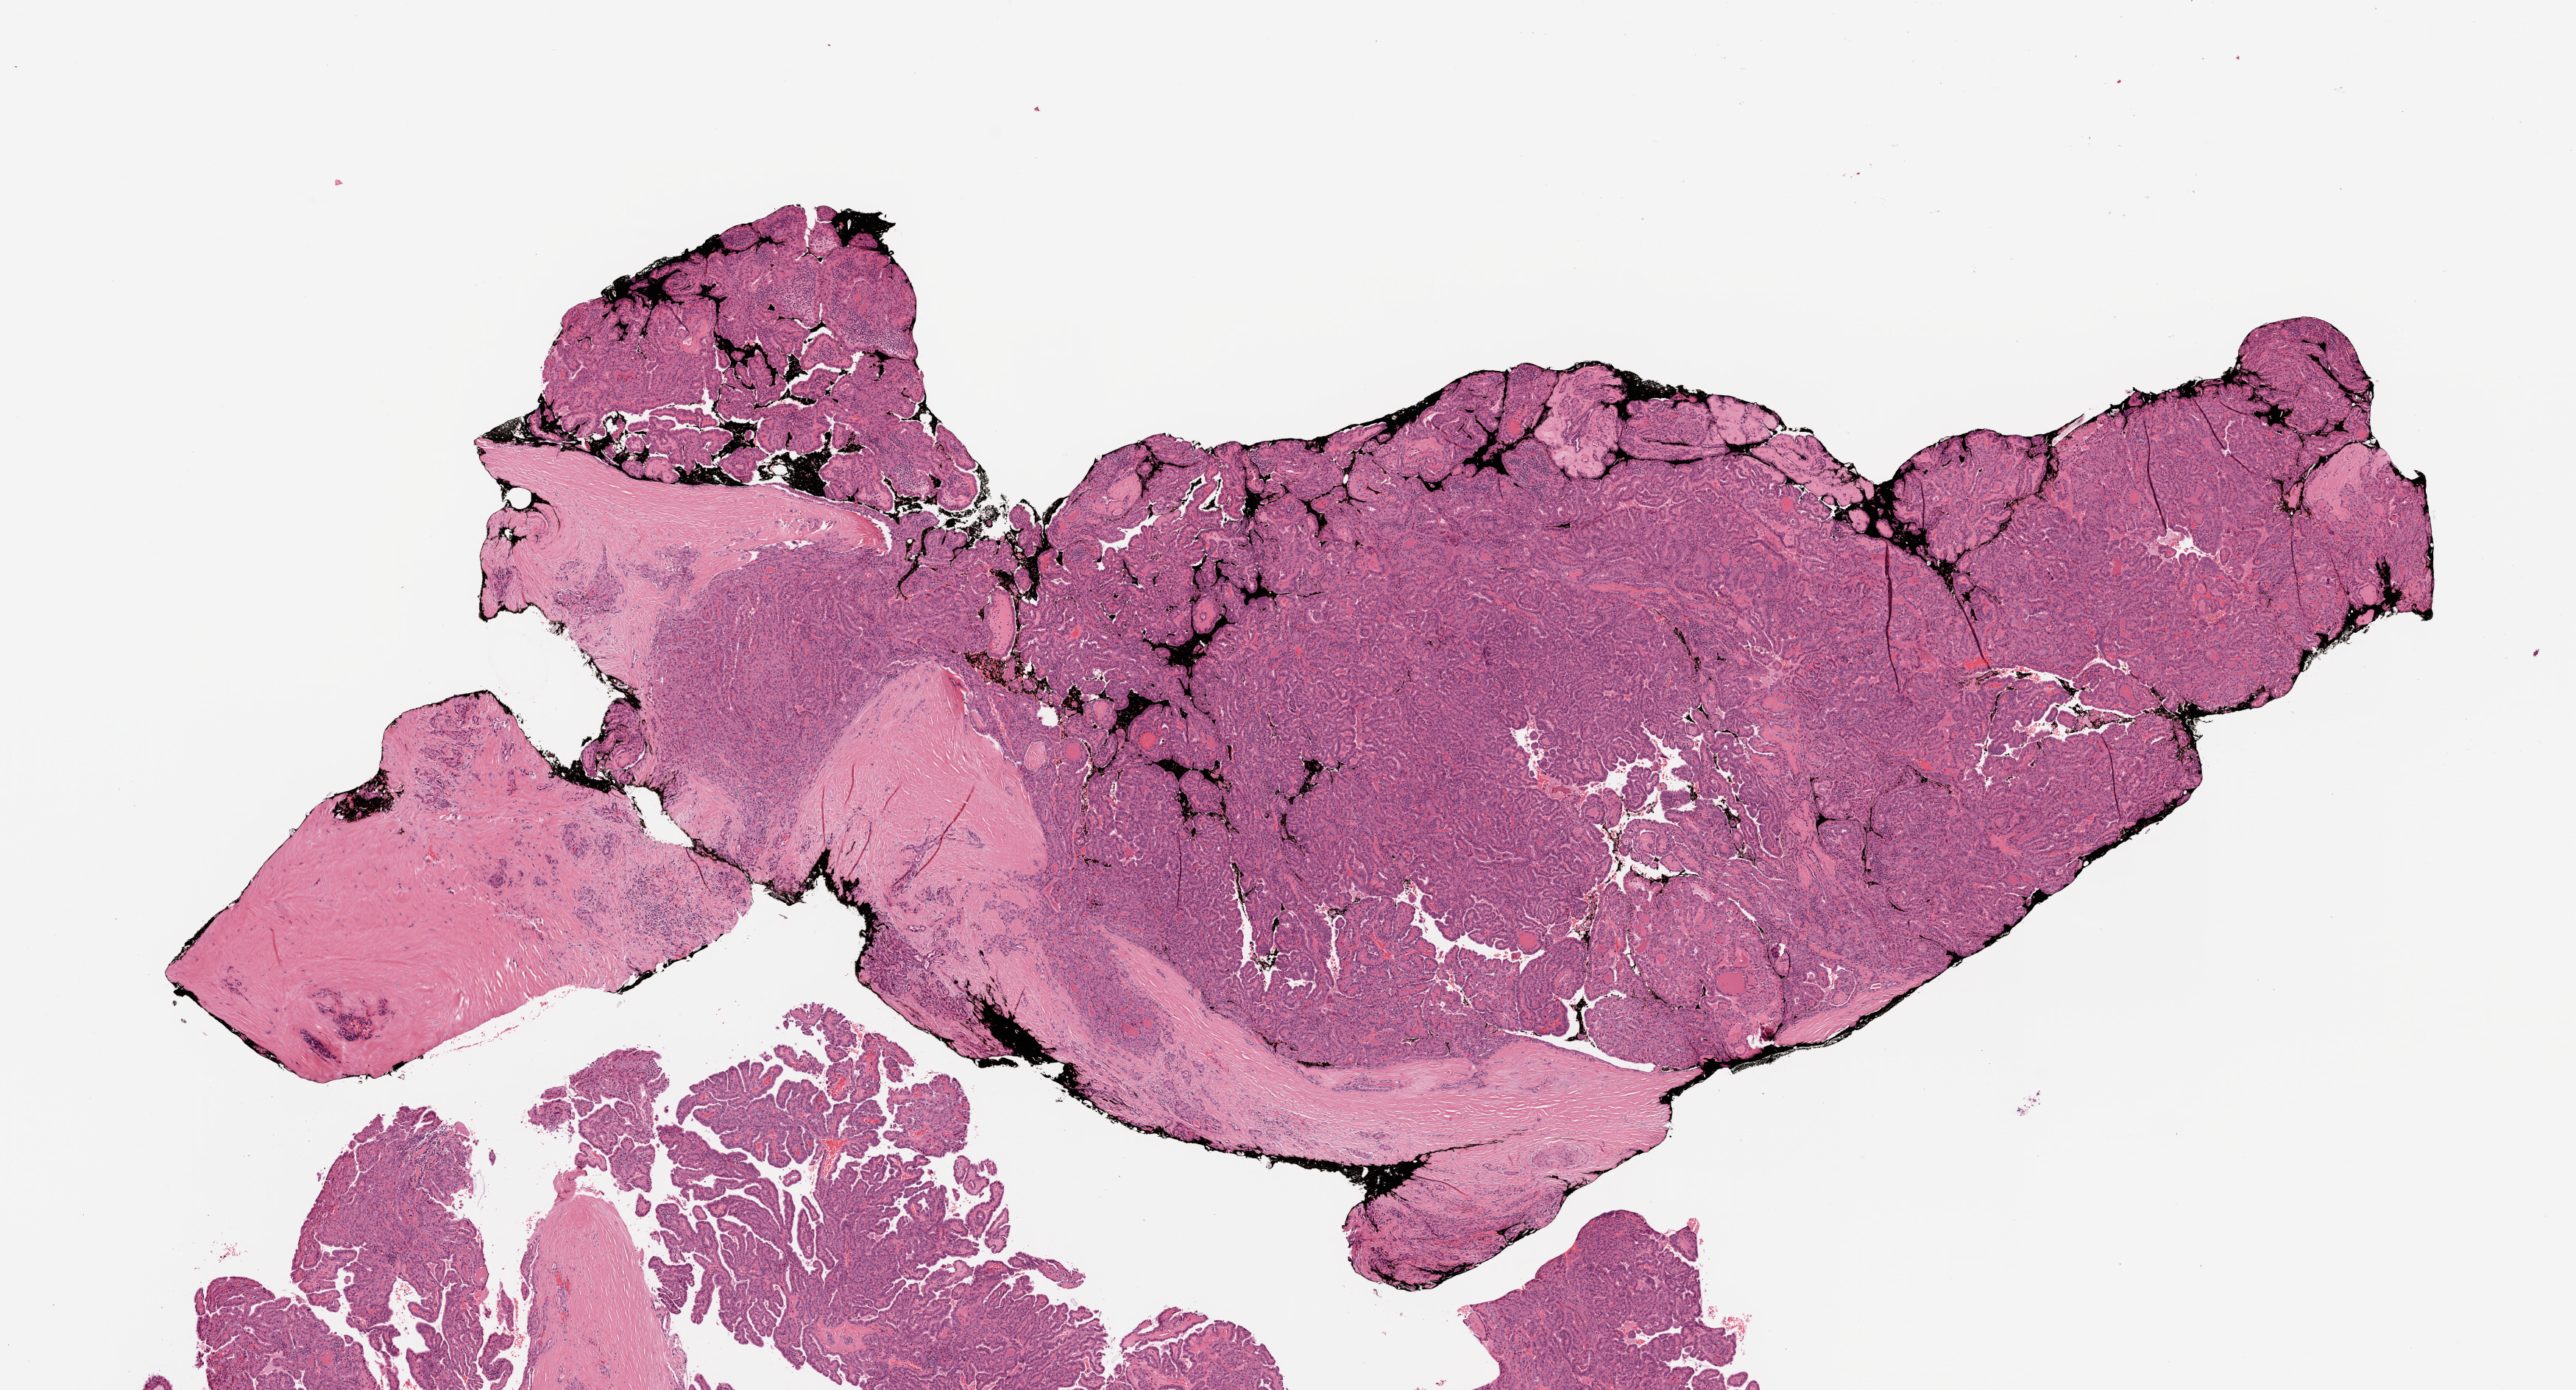
Digitized Hematoxylin and eosin (H&E) stained tissue section (whole slide), shown as a low-resolution overview of the whole scanned area (about 14.0 x 7.6 mm, from a 20x scan); formalin-fixed paraffin-embedded (FFPE) diagnostic section; thyroid, primary tumour sample. Female patient; age at initial diagnosis 42 years.
TNM: T2 N0 MX. Pathologic diagnosis: Papillary adenocarcinoma, NOS (thyroid gland). AJCC pathologic stage: I.